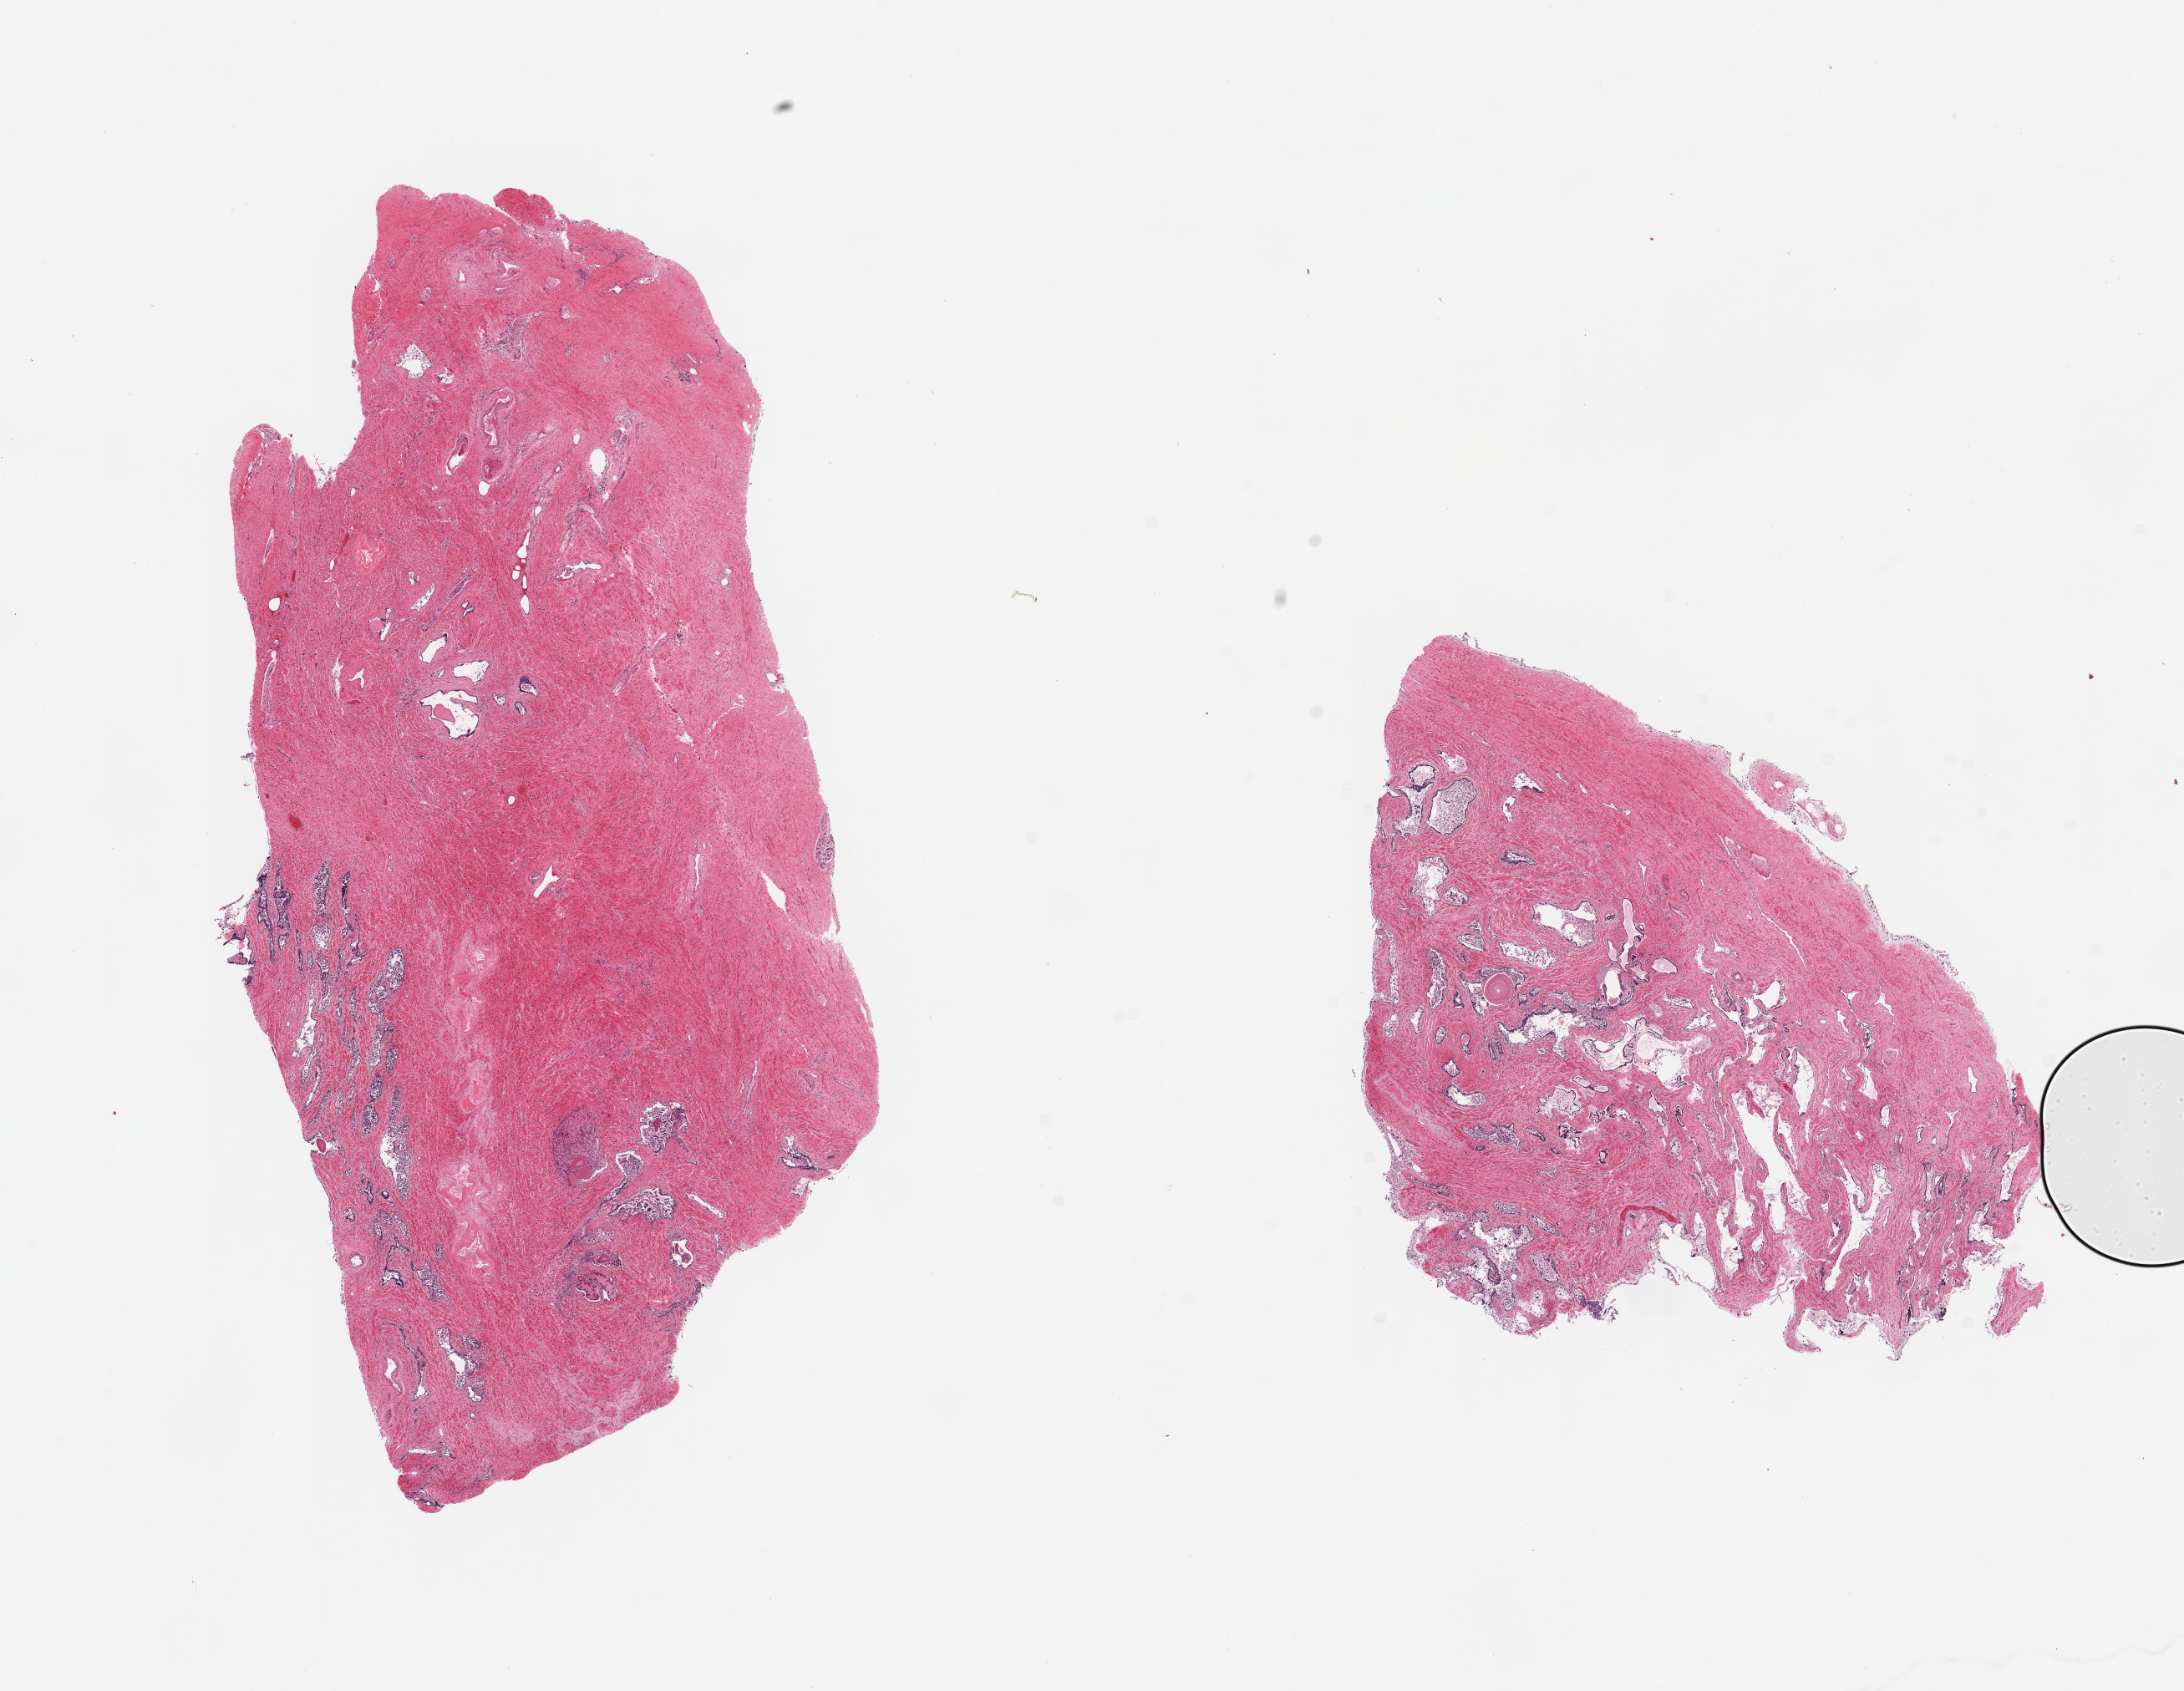
Digitized H&E-stained section, brightfield, whole scanned area (about 20.7 x 16.0 mm, slide scanned at 20x) shown as a low-resolution overview, PAXgene-fixed paraffin-embedded (PFPE) section, target tissue: prostate, tissue donor sample. Donor sex: male.
- review note (as recorded): 2 pieces, glandular elements with advanced autolysis